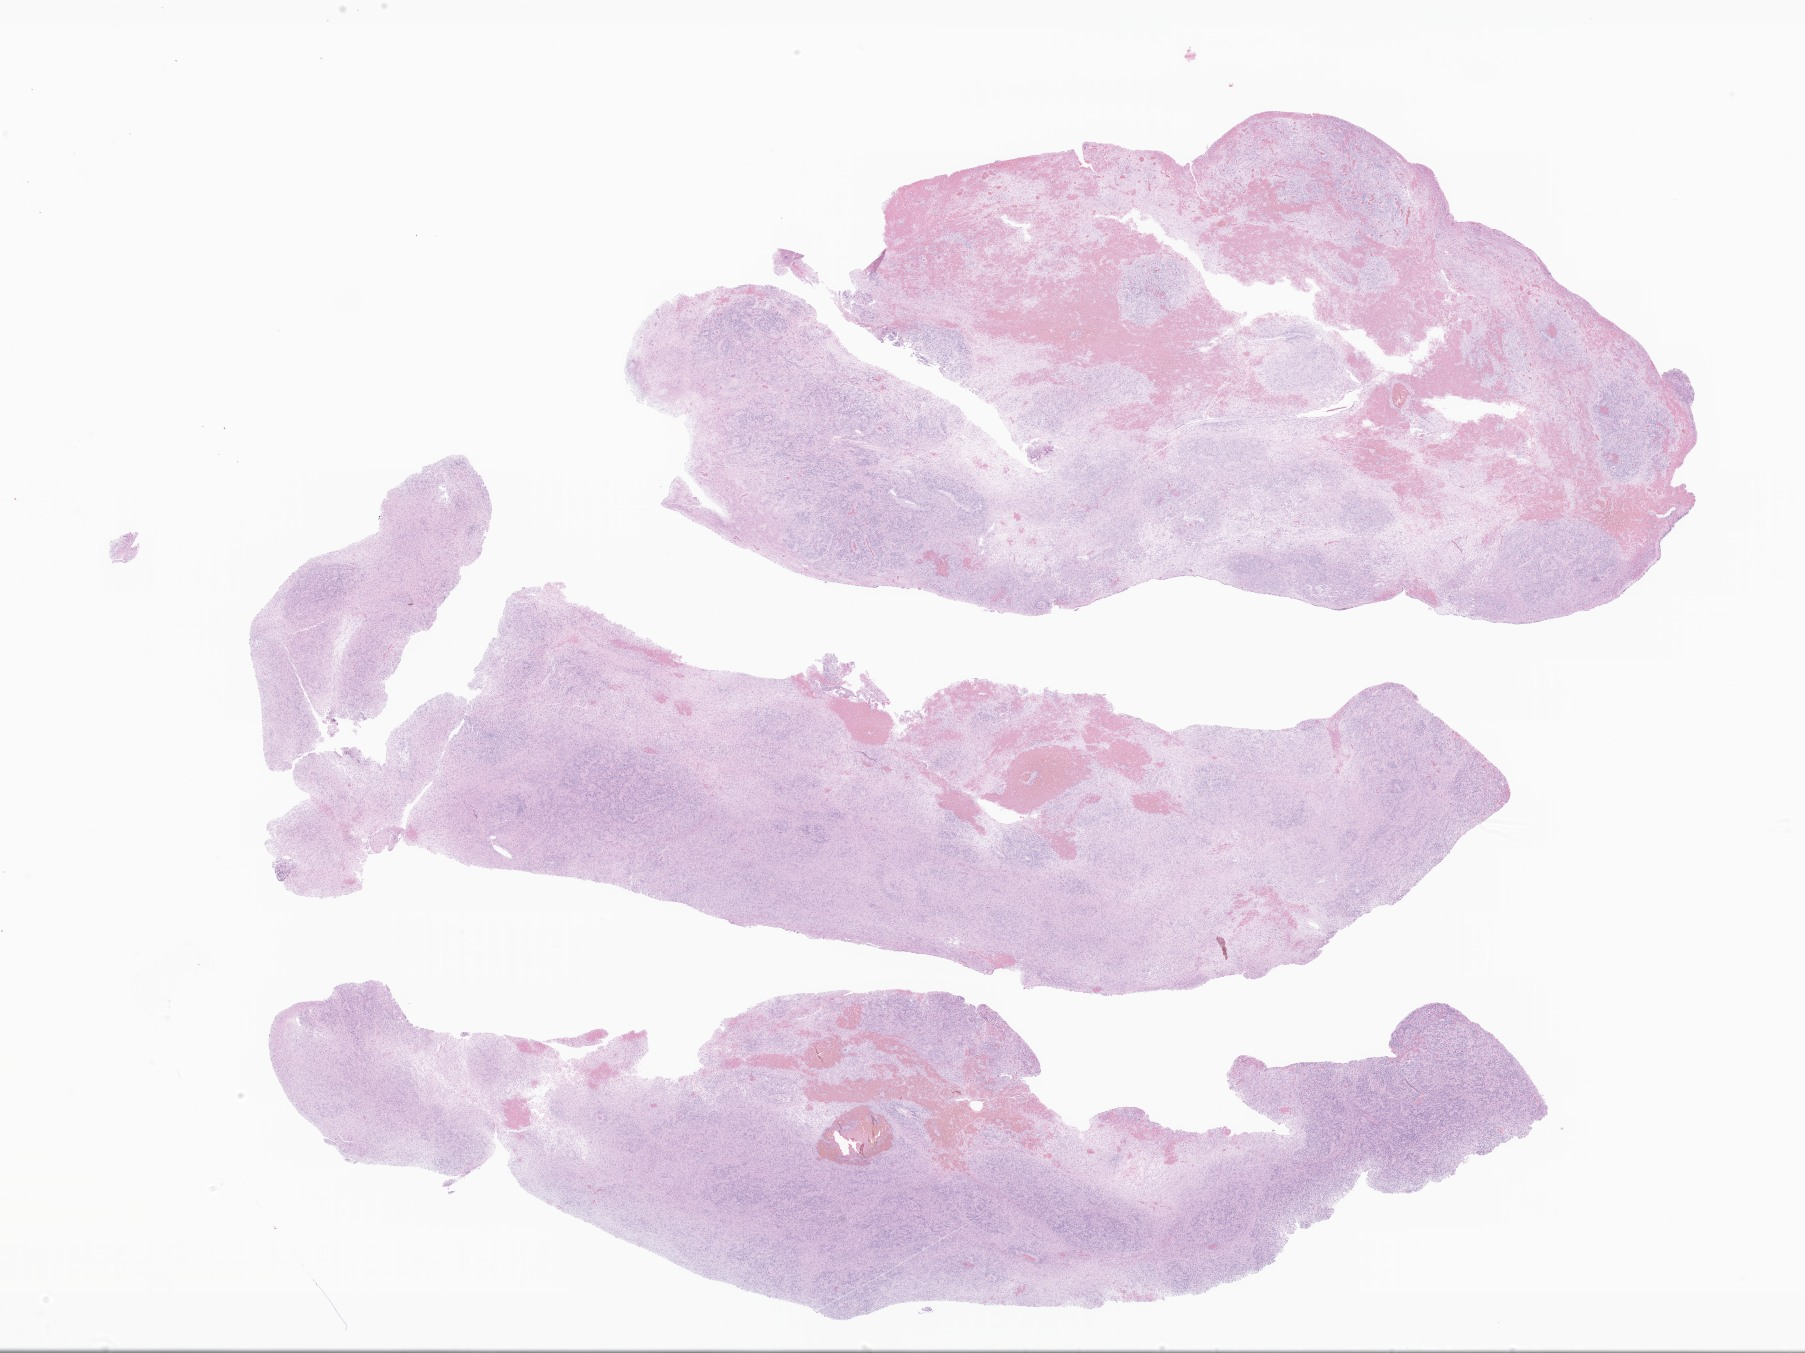
Haematoxylin and eosin whole-slide image of tumor tissue from the cerebral ventricle — a low-resolution overview of the entire scanned area, about 30.4 x 22.8 mm; formalin-fixed paraffin-embedded section. Patient: female, age 587 days (about 1.6 years).
Recorded diagnosis: Ependymoma, NOS.